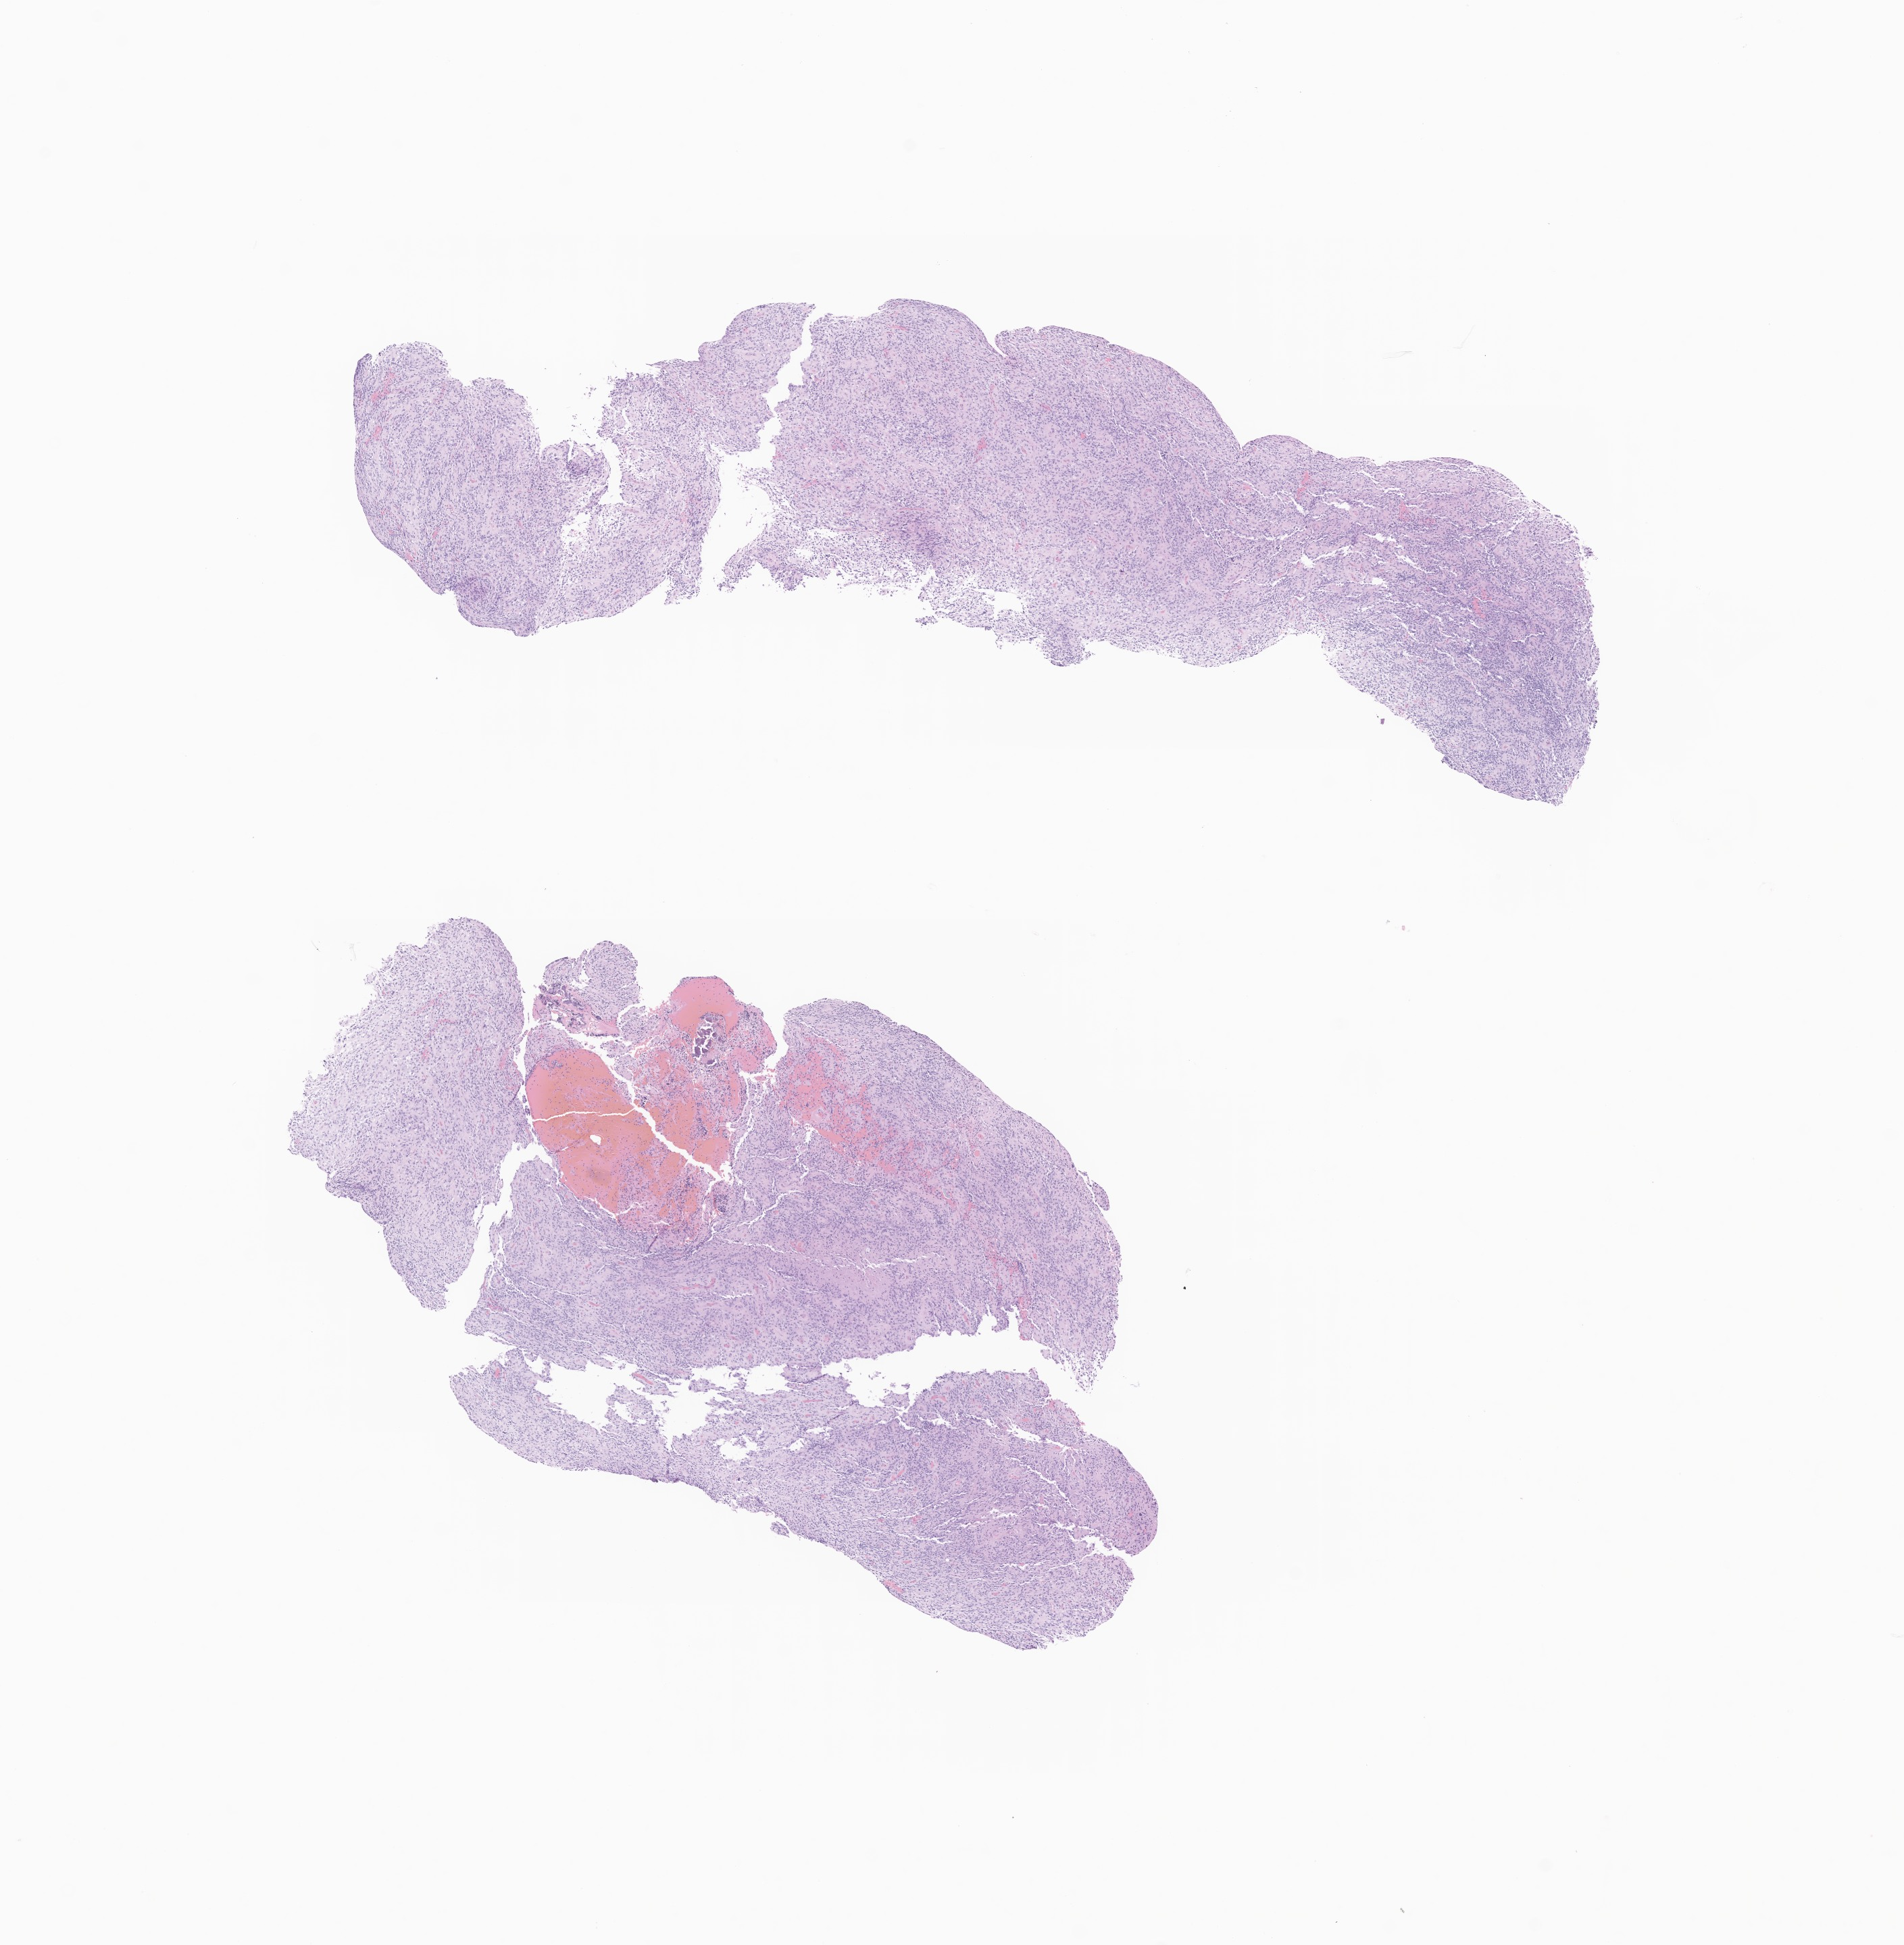
Digitized hematoxylin and eosin (H&E)-stained section of tumor tissue from the brain, shown as a low-resolution overview of the whole scanned area (about 11.9 x 12.1 mm), FFPE section. Patient male; age 288 months.
Recorded diagnosis: Glioma, malignant.